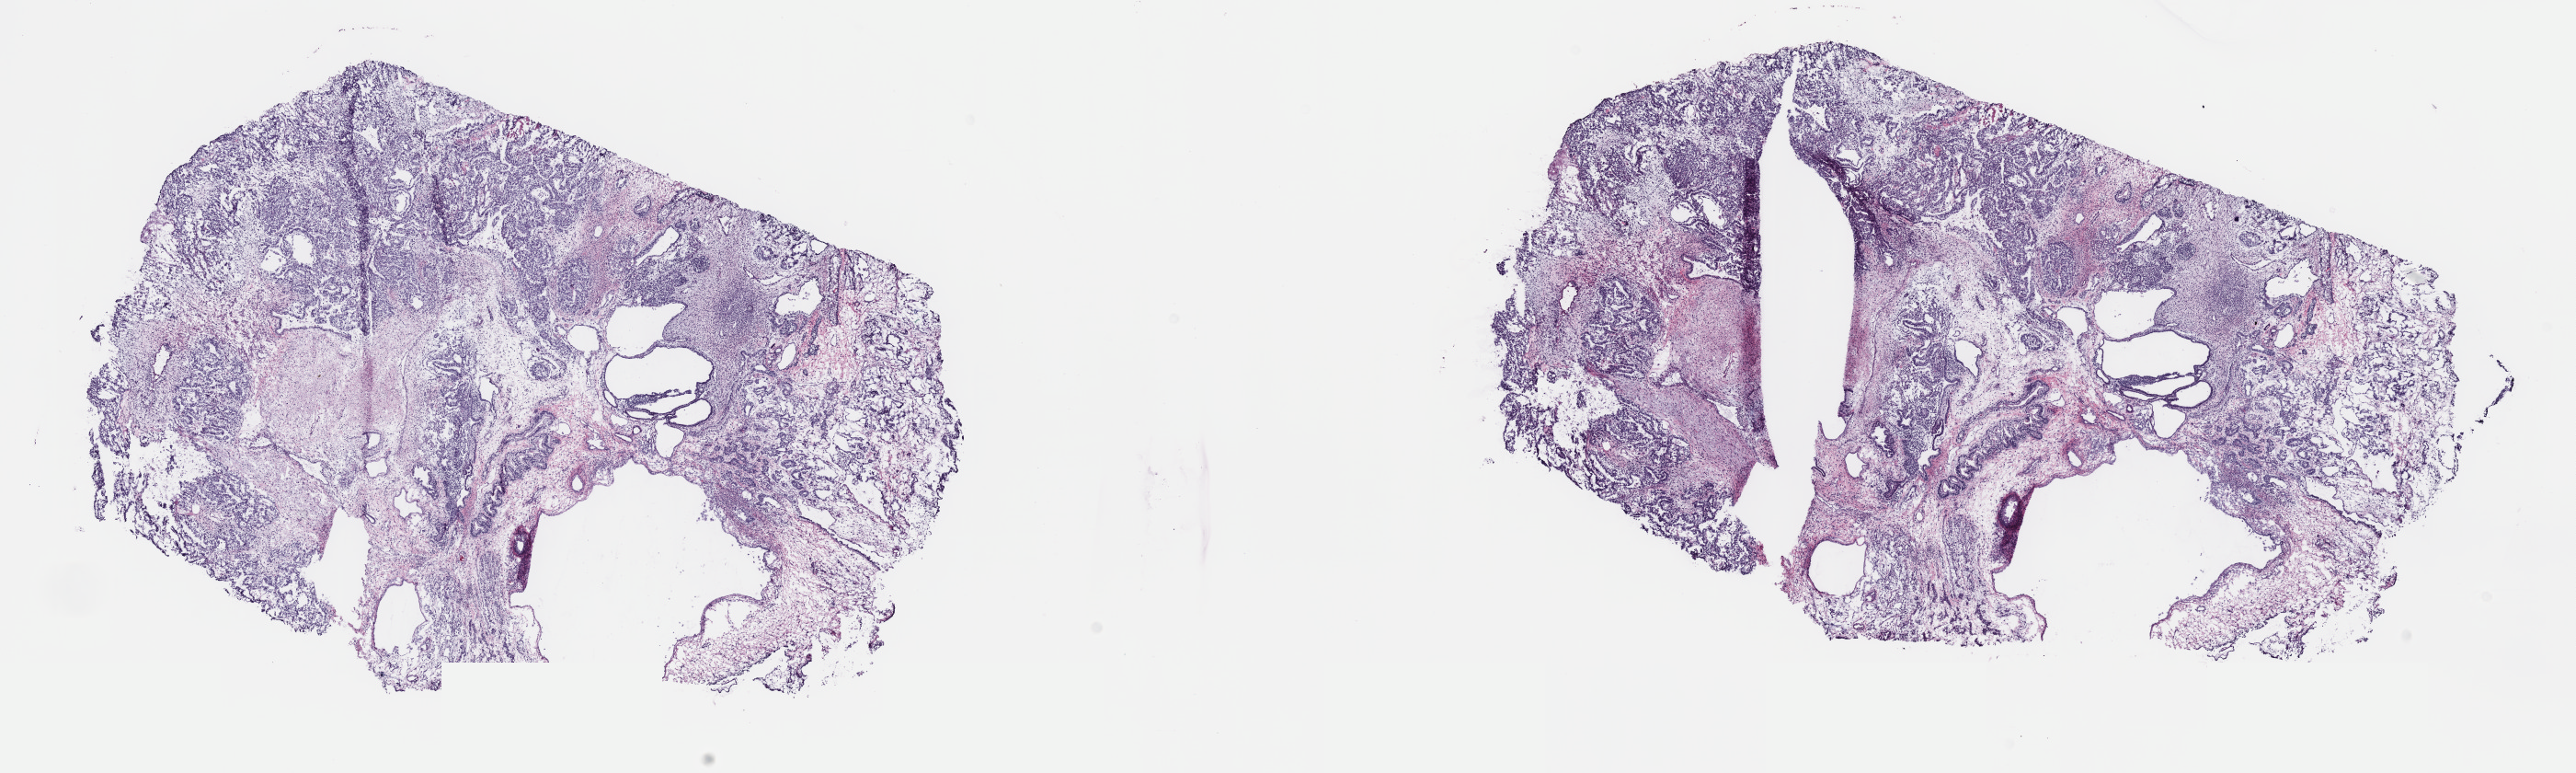
Hematoxylin and eosin (H&E) stained whole-slide image, low-resolution overview of the scanned area, about 22.7 x 6.8 mm (from a 40x scan), frozen section from the top of the tissue portion, testis, primary tumour sample. Male, age 32 years at initial diagnosis. Pathologist review of this section (percent, as recorded): tumour cells 100%, tumour nuclei 95%, normal cells 0%, stromal cells 0%, necrosis 0%. Infiltration values recorded for this section: lymphocyte infiltration 0%, monocyte infiltration 0%, neutrophil infiltration 0%.
Diagnosis: Mixed germ cell tumor. AJCC pathologic stage: III.